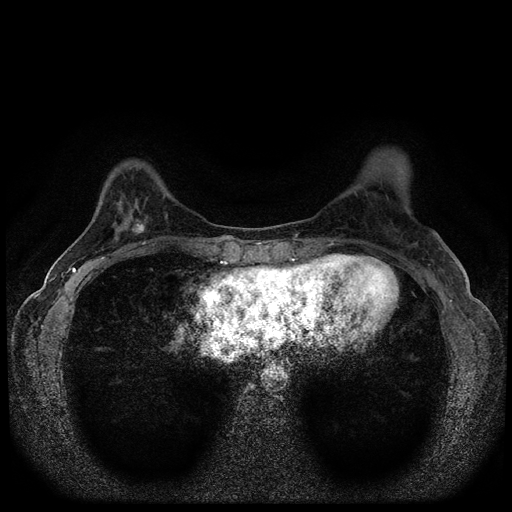
Breast MRI (dynamic contrast-enhanced, multi-phase), one axial slice; slice 32 of 116 in the series (ordered by position); dynamic contrast-enhanced series, time point 2 of 5 at this slice position (early post-contrast); 1.5 T; TE 2.7 ms, TR 5.6 ms; 512 × 512 image matrix, field of view 310 × 310 mm. Female patient, age 40 years.
Annotated regions visible in this slice (semi-automatically segmented with operator editing):
- breast lesion (labelled benign in the annotation): bounding box [x1, y1, x2, y2] px = [122, 214, 148, 237]